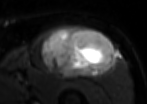
MRI of an extremity soft-tissue mass, one axial slice. T2-weighted fat-saturated. MR volume resampled by the dataset authors to the PET/CT grid (not the native acquisition matrix). 3.27 mm slice thickness. 147 × 104 image matrix, field of view 144 × 102 mm. Male patient. Case-level facts recorded for this patient, not image findings: histological type: extraskeletal osteosarcoma; grade: high; site of the primary tumour: thigh.
Structures marked on this image (expert contour drawn on MRI and transferred to this co-registered scan by the dataset authors):
- gross tumour volume (mass): box from (x=40, y=26) to (x=116, y=77) px